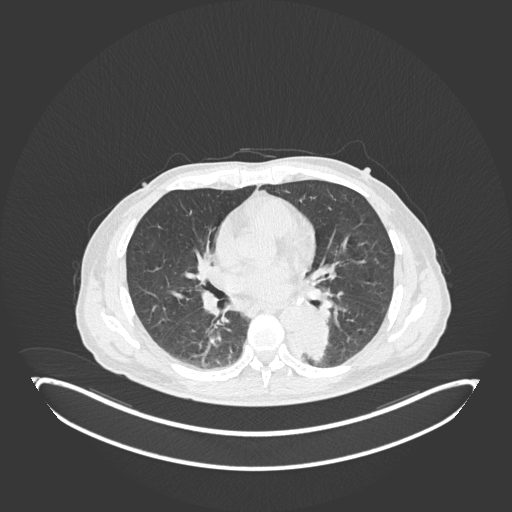
Chest CT, one axial slice; slice 97 of 251 in the series (ordered by position); reconstruction kernel B30f; lung window (W 1500 / L -600 HU); 512 × 512 image matrix. Patient: male, 72 years. Case-level facts recorded for this patient, not image findings: clinical TNM (as recorded): T2b N0 M1.
Structures marked on this image (bounding box drawn by a radiologist):
- lung tumour (recorded histology: adenocarcinoma): bounding box <285,319,332,371> (left, top, right, bottom; pixels)